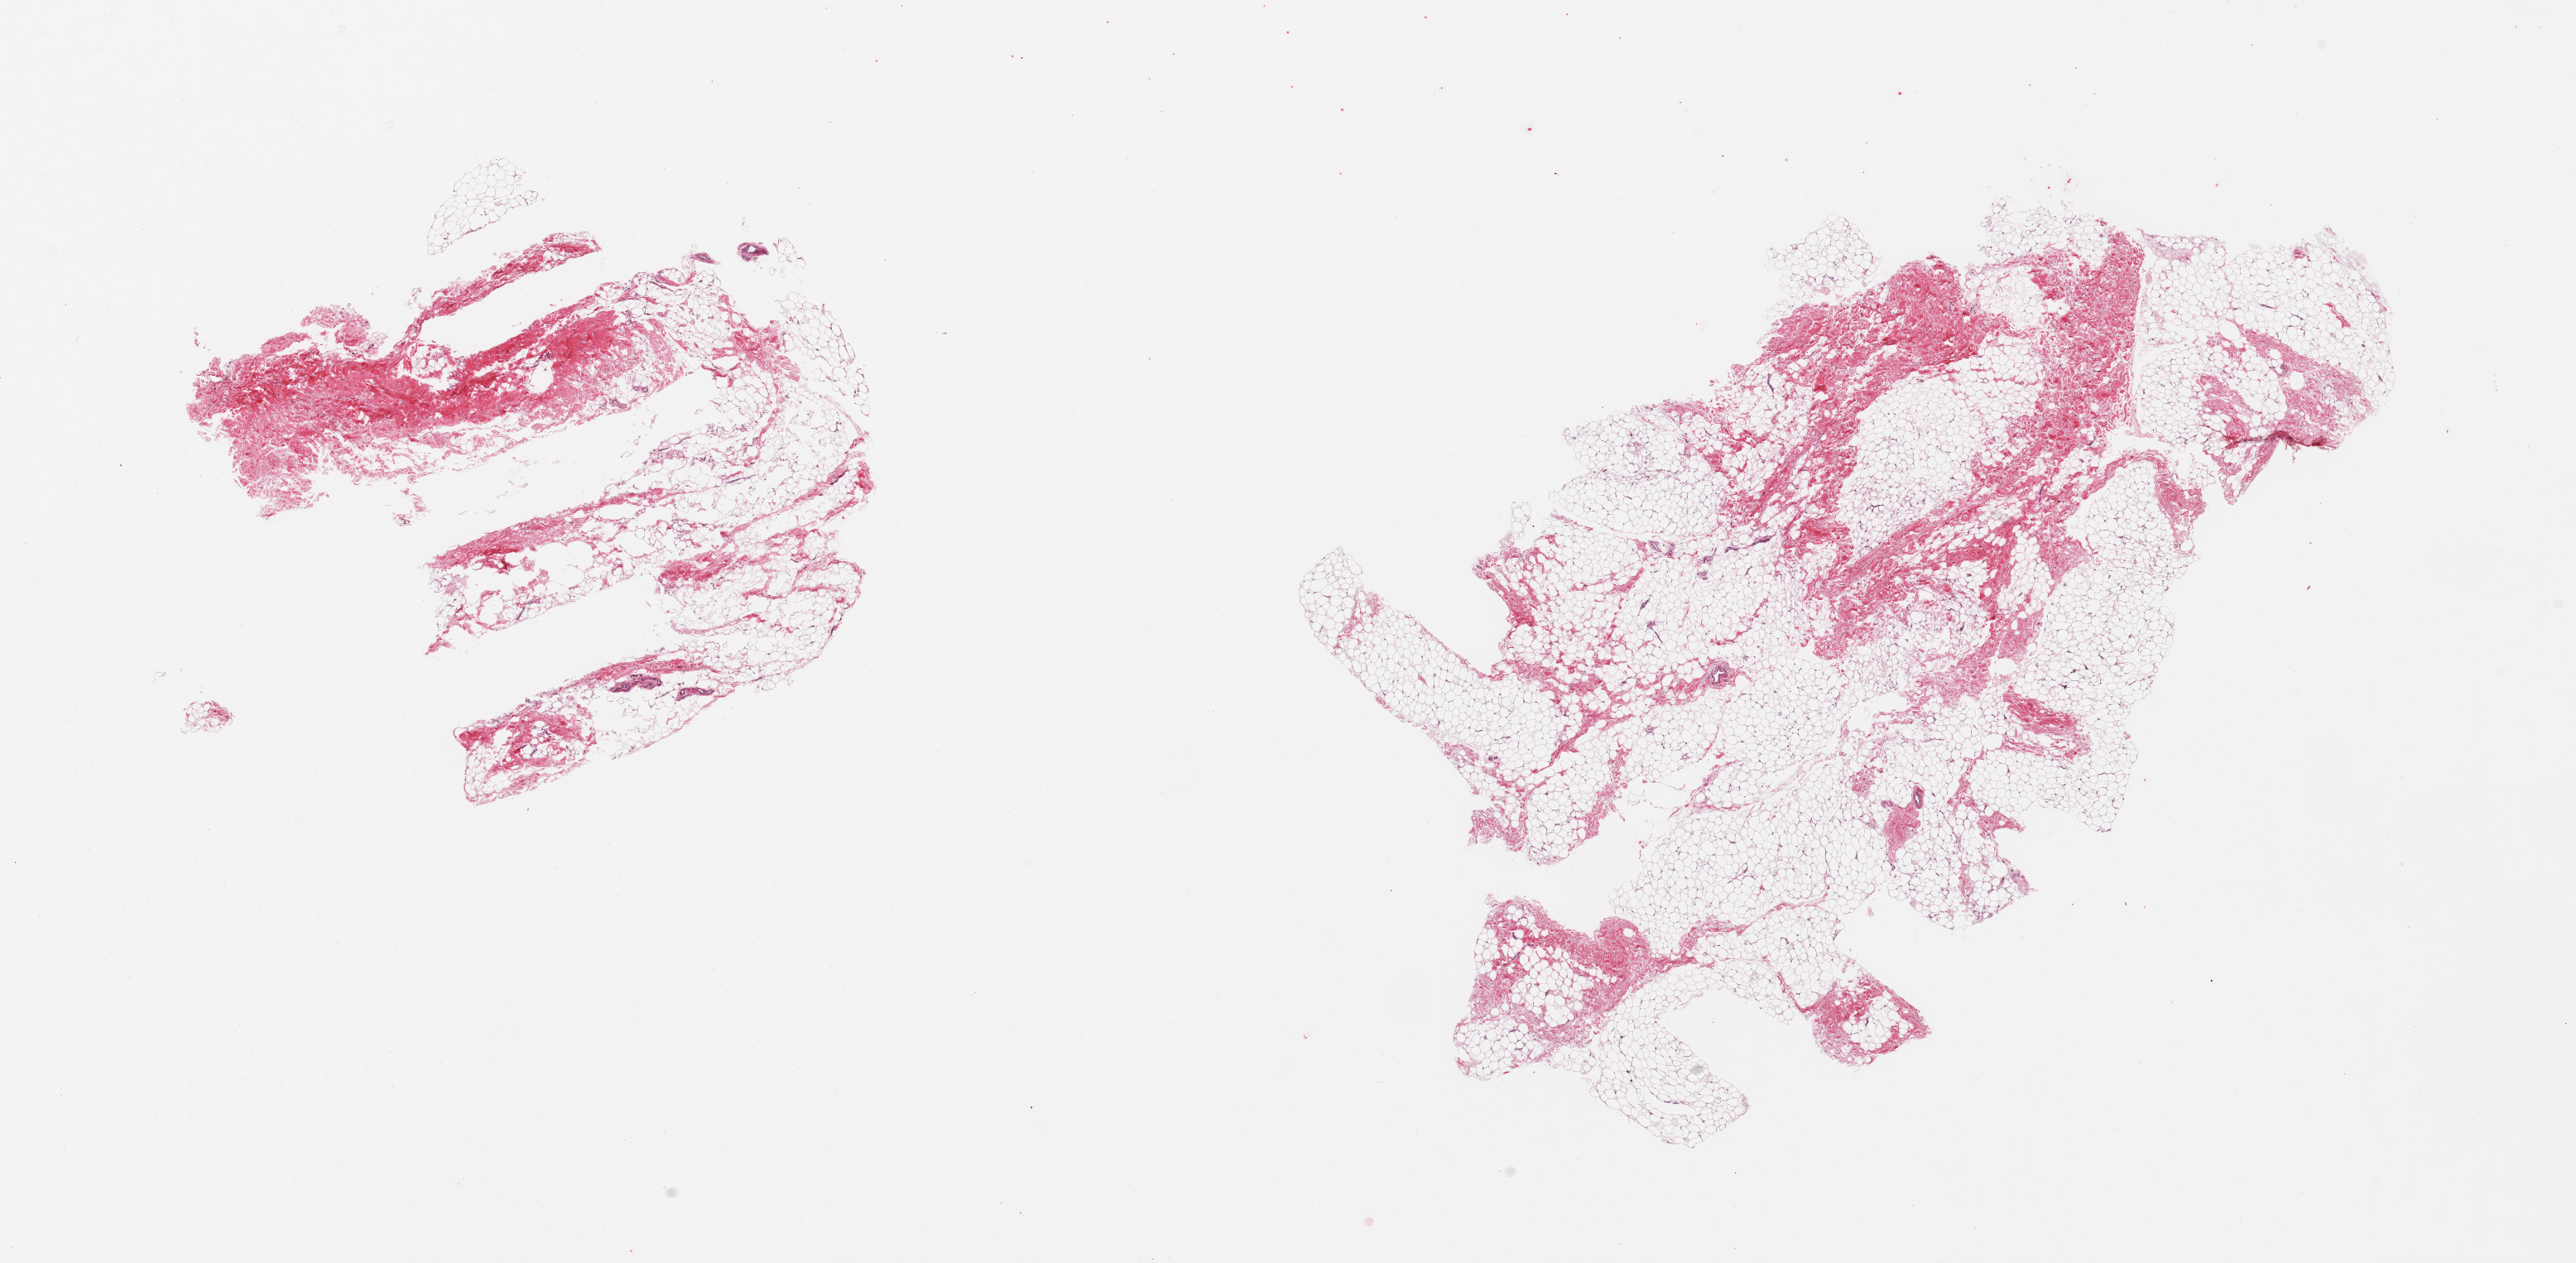
Digitized haematoxylin and eosin-stained section — a low-resolution overview of the entire scanned area, about 24.6 x 12.1 mm; PAXgene-fixed, paraffin-embedded tissue; section of breast (target tissue); donor tissue sample. Donor: male.
Review note (as recorded): 2 pieces; predominanlty fat with 20-30% fibrous tissue, no ductal elements seen.